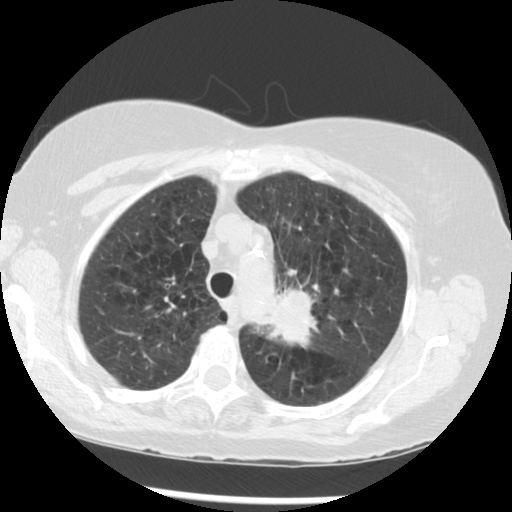
Axial slice from a low-dose chest CT screening exam, third annual screen, lung window (W 1500 / L -600 HU), 512 × 512 image matrix, field of view 330 × 330 mm. Female participant, aged 70 years at enrolment. Current smoker at enrolment.
- Expert reader's lesion annotation, bounding box [x1, y1, x2, y2] px = [262, 272, 357, 361].
- Screening reader's record for this exam (one nodule recorded; not confirmed to be the boxed lesion): non-calcified nodule or mass ≥4 mm, left upper lobe, 32 × 26 mm, spiculated (stellate) margins, soft tissue attenuation, pre-existing on the prior screen: yes; interval growth: yes.
- Later outcome: lung cancer diagnosed 24 days after this screen — neoplasm, malignant, left upper lobe, stage IIIB (AJCC 6th edition), 40 mm at pathology.